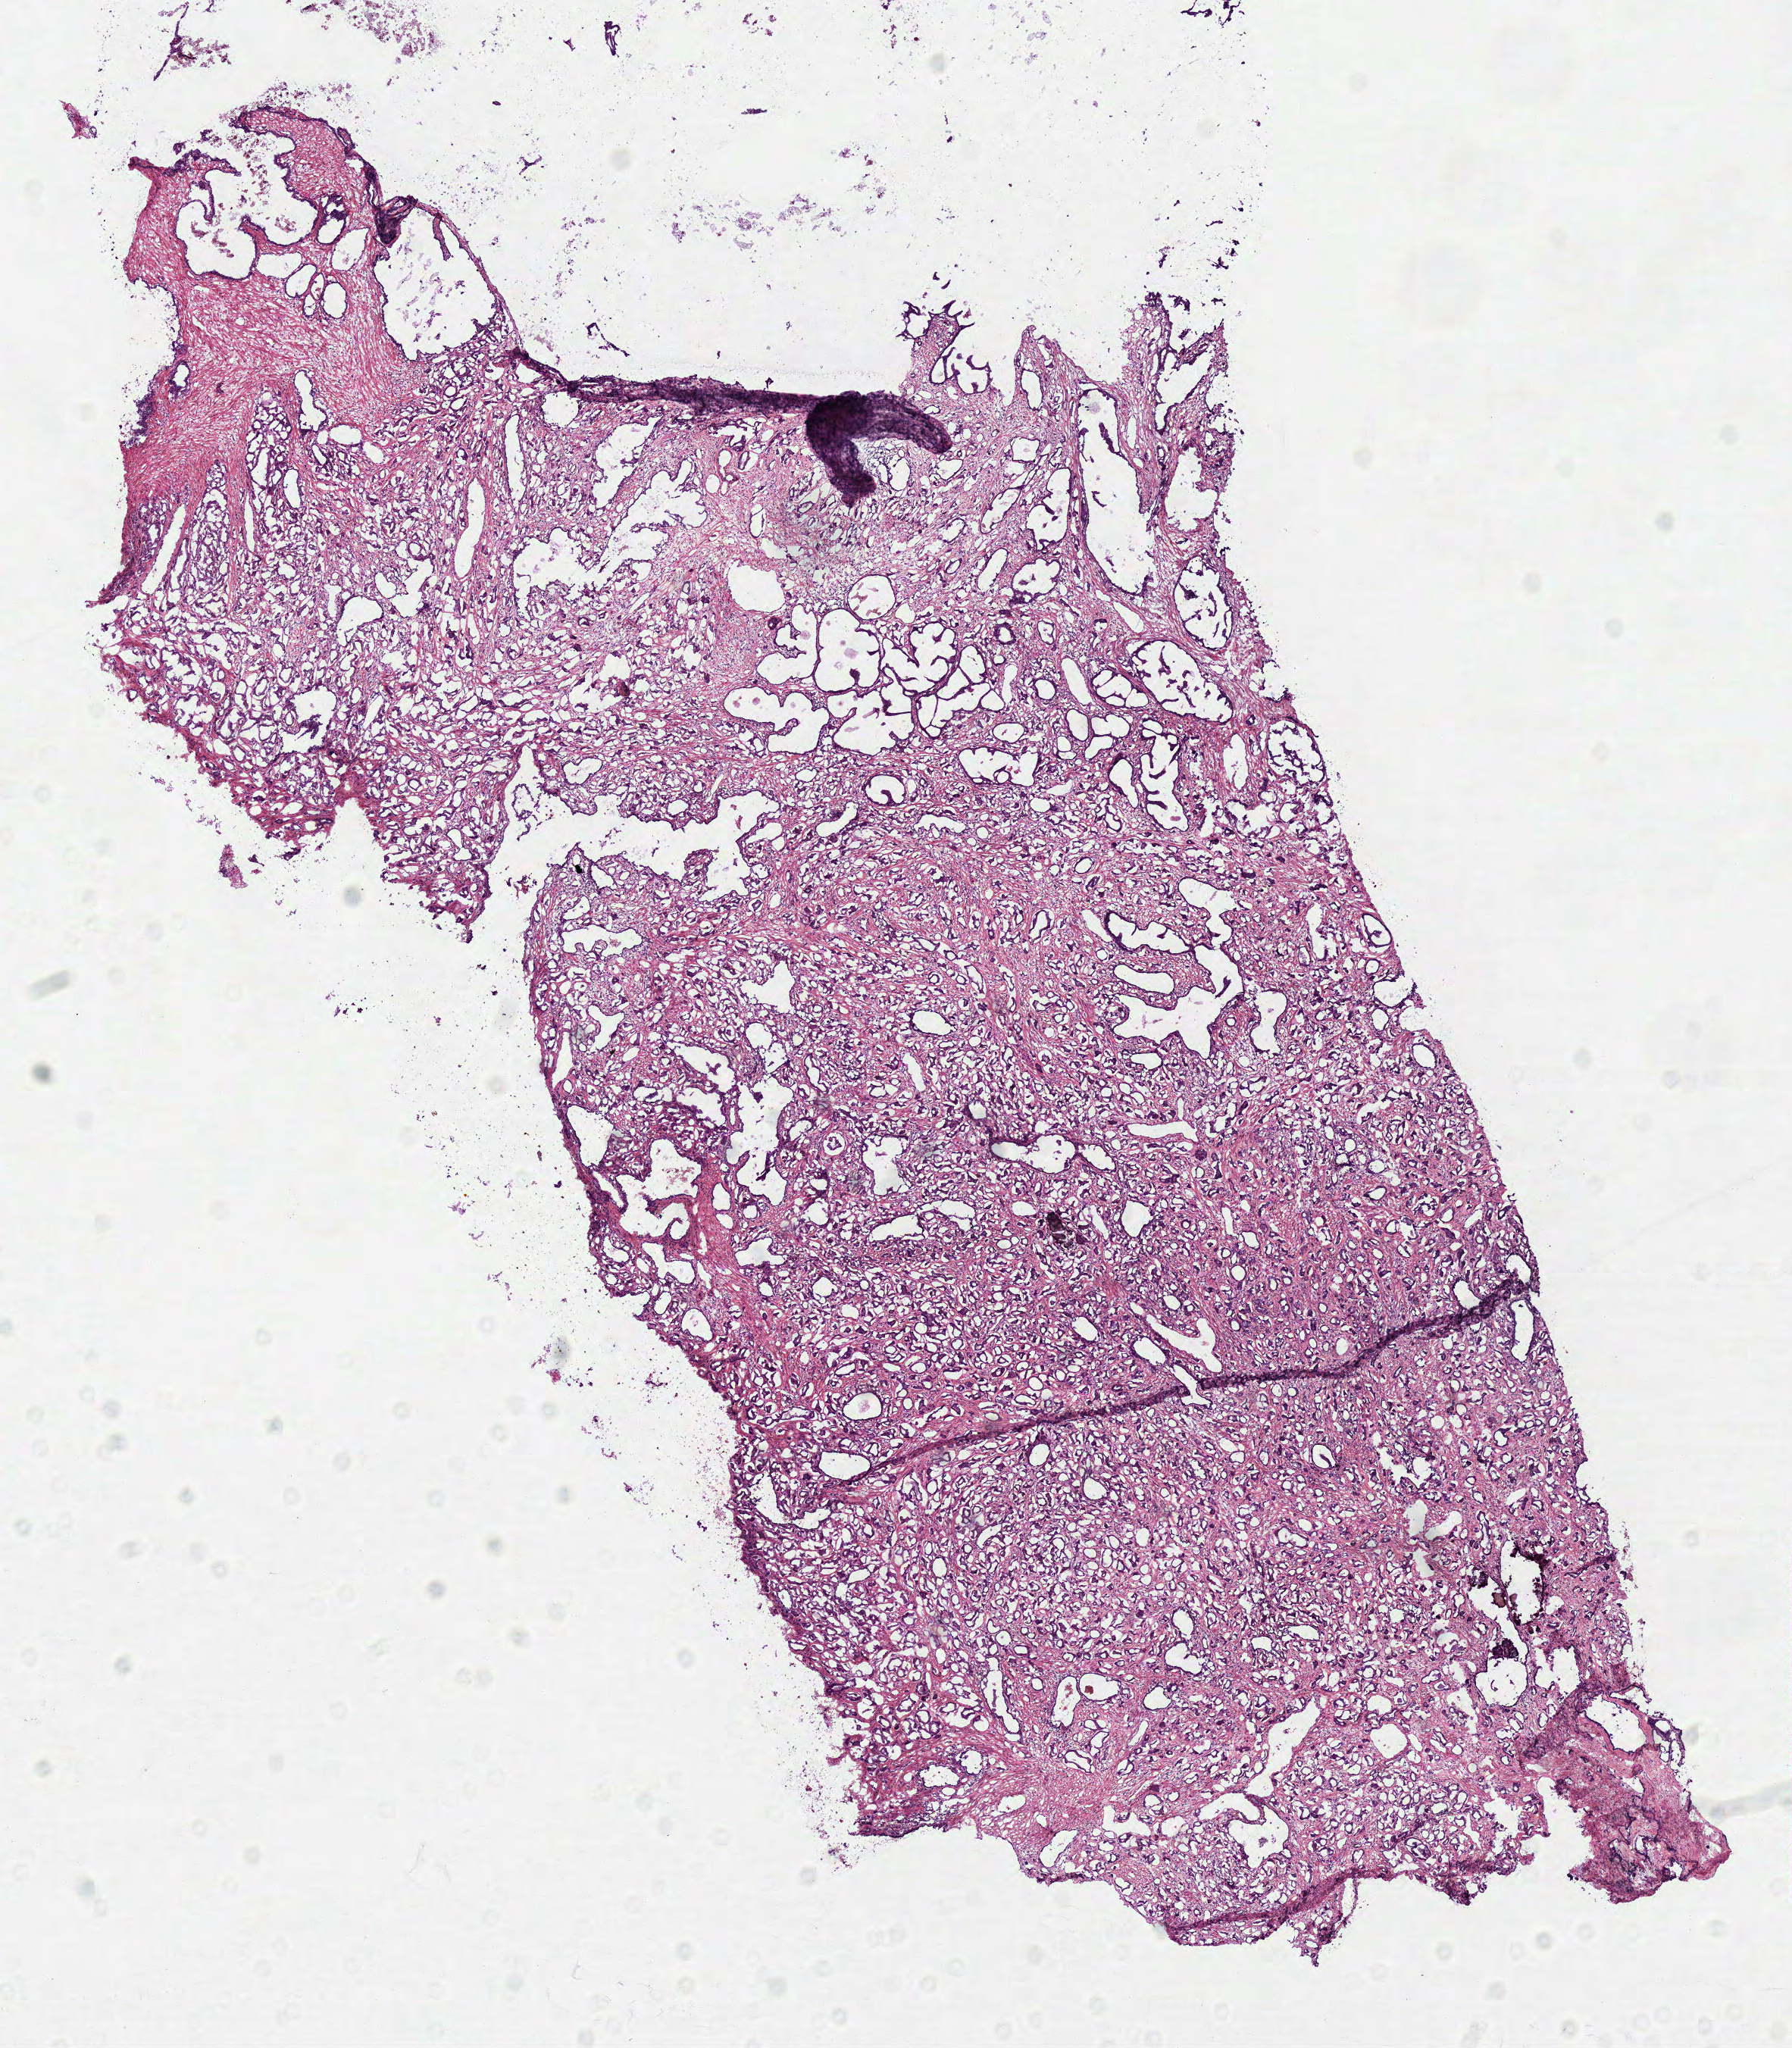
Whole-slide histology image, H&E-stained, shown as a low-resolution overview of the whole scanned area (about 9.3 x 10.6 mm, acquisition: 40x scan); frozen section from the top of the tissue portion; primary tumour sample from the prostate. Male patient; age at initial diagnosis 68 years. Gleason score: 7 (3+4). Slide review estimates, as recorded: tumour cells 75%, tumour nuclei 80%, normal cells 12%, stromal cells 13%, necrosis 0%. Inflammatory infiltration, as recorded: lymphocyte infiltration 2%, monocyte infiltration 0%, neutrophil infiltration 0%.
• diagnosis: Acinar cell carcinoma (prostate gland)
• lymph nodes positive (case pathology): 0 of 15 examined
• laterality: bilateral